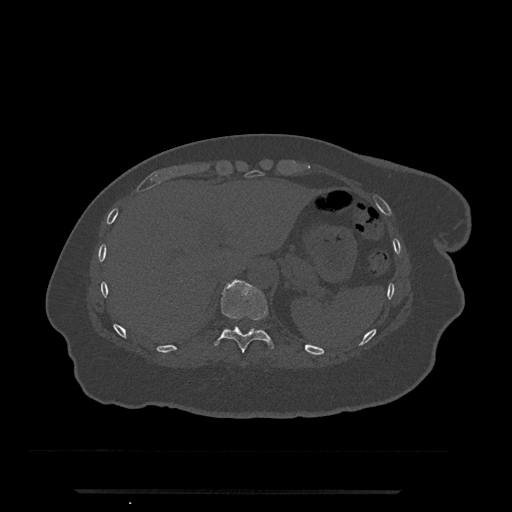
CT including the spine, one axial slice; position 276 of 797 along the scan axis; reconstruction kernel Br40s/3; bone window (W 1800 / L 400 HU); 0.5 mm slice thickness; 512 × 512 image matrix, field of view 440 × 440 mm. Female patient, age 51 years. From the clinical record (not read from this slice): primary cancer: neuro; vertebrae with lytic lesions (as recorded): T8.
Structures marked on this image (semi-automatic segmentation, software-assisted and operator-edited):
- T10 vertebra: box from (x=213, y=279) to (x=274, y=353) px